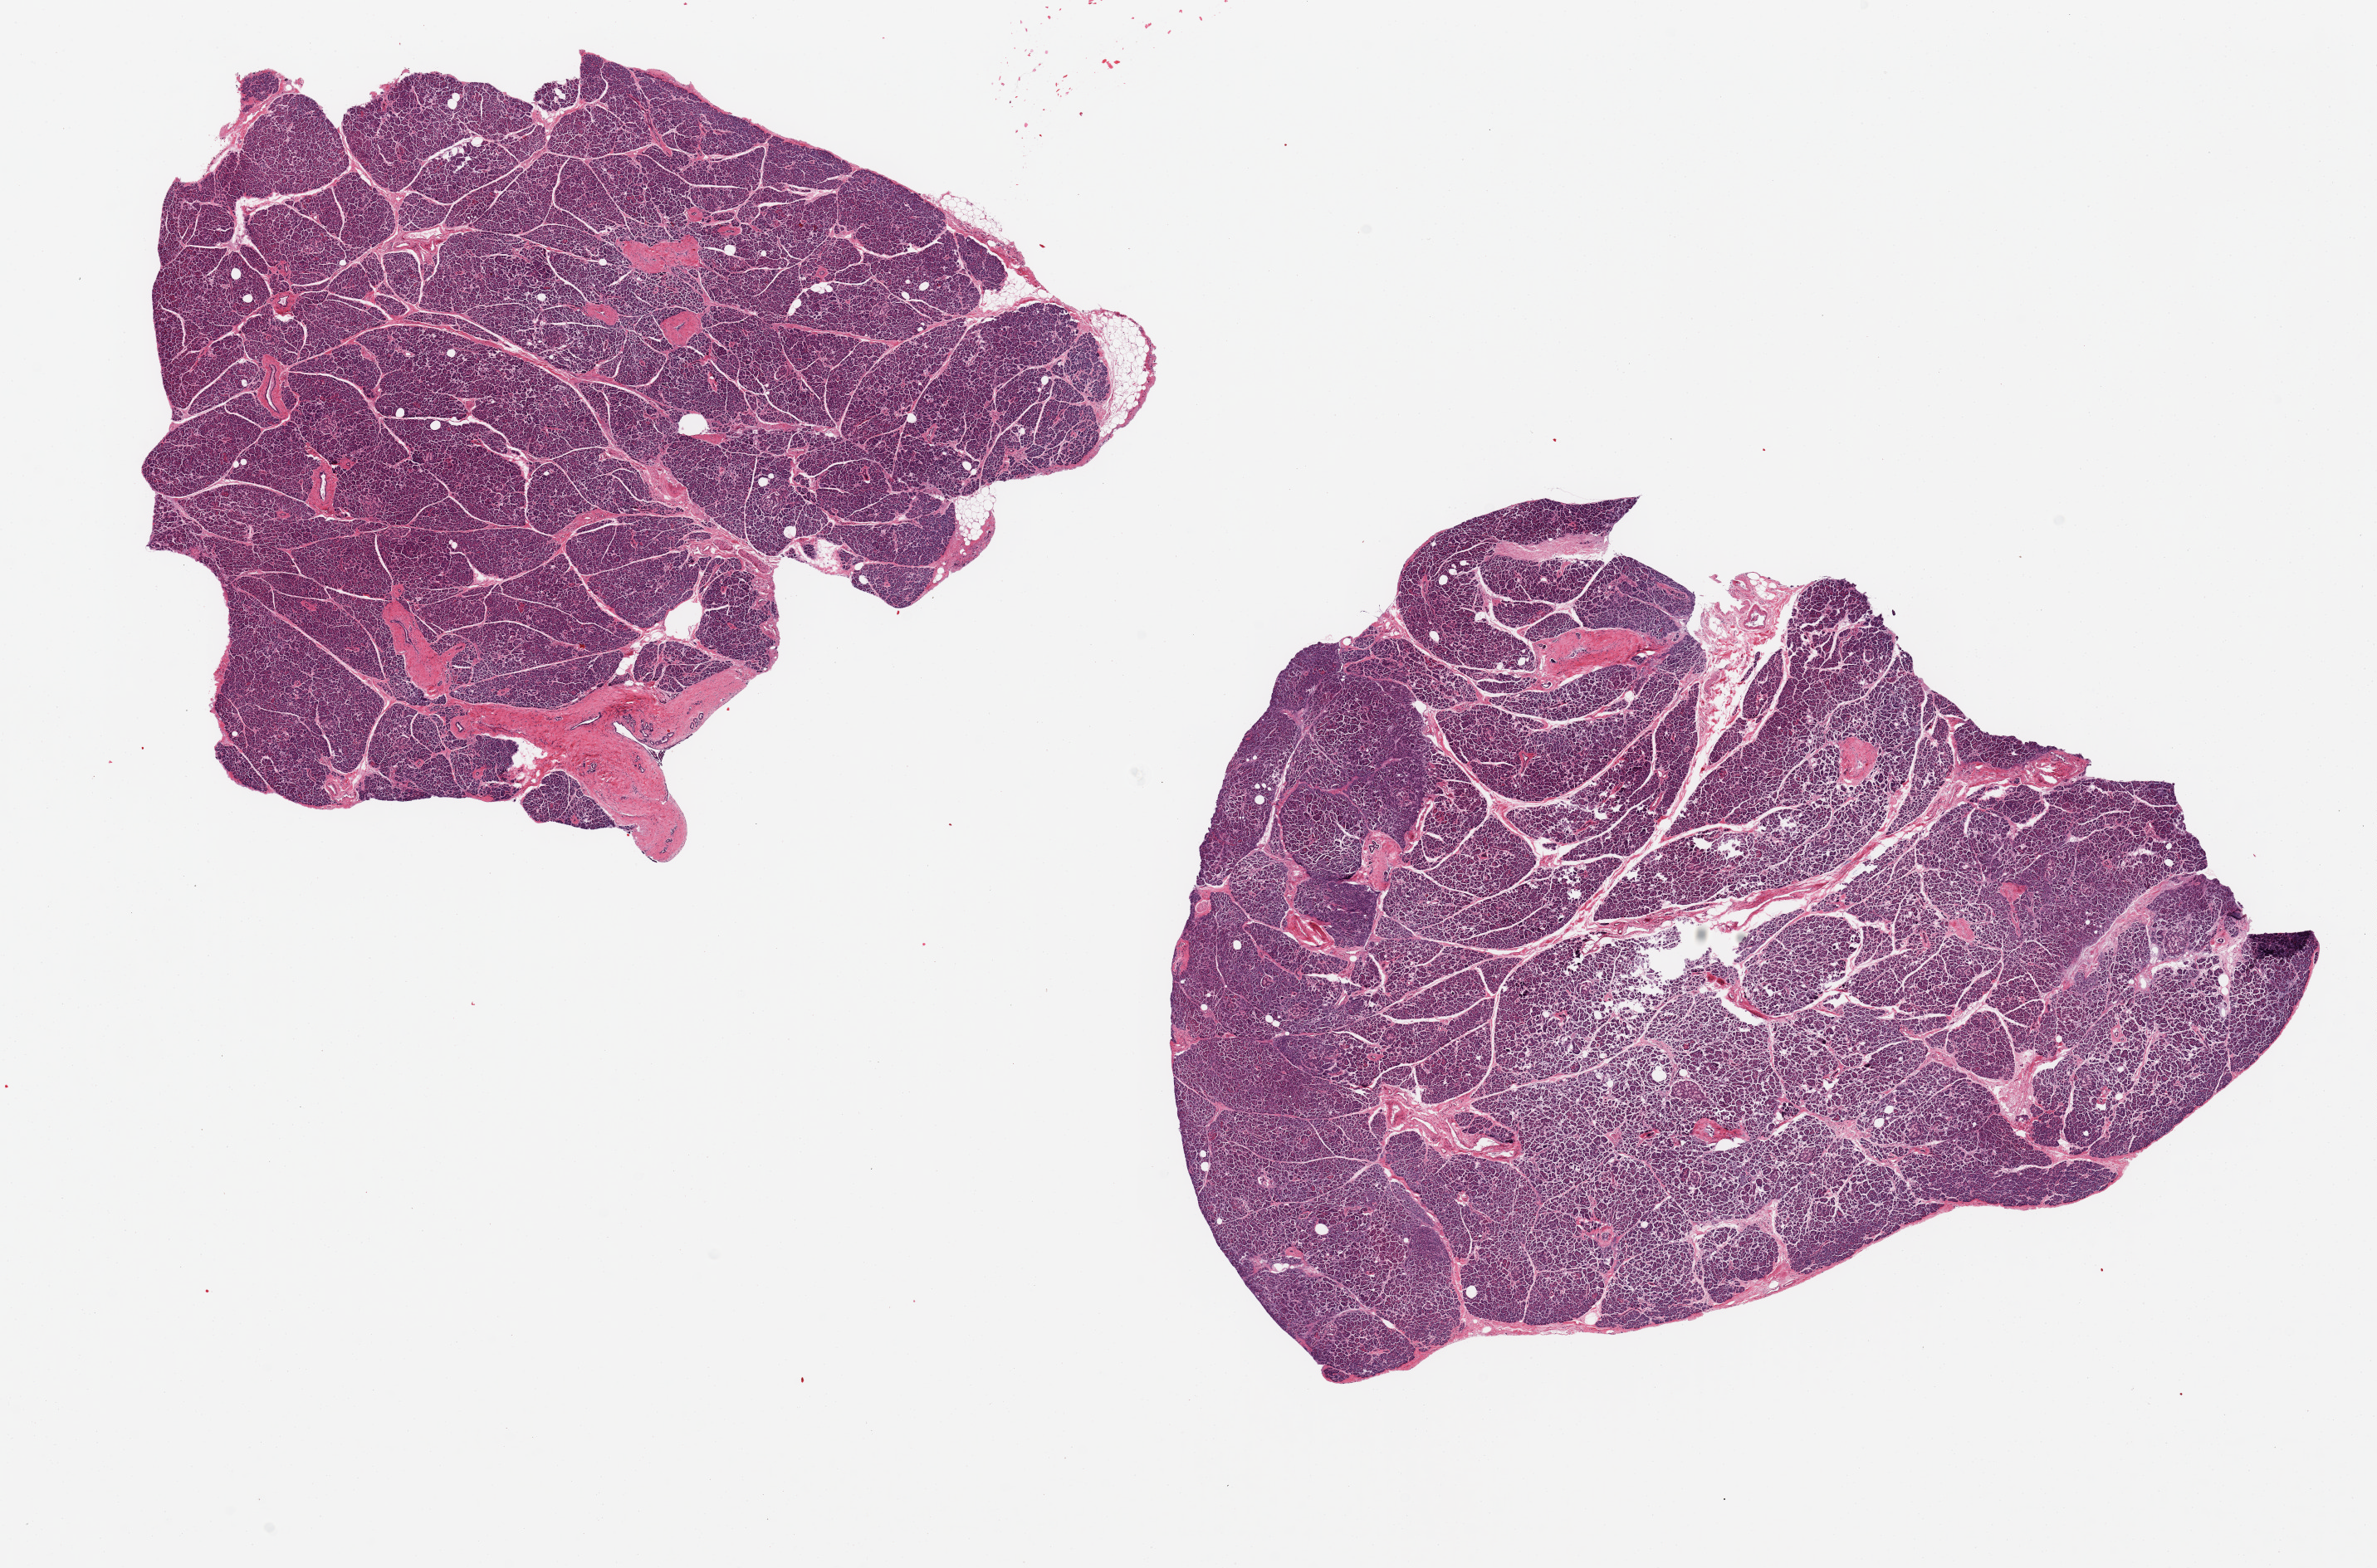
Digitized haematoxylin and eosin-stained section, brightfield, a low-resolution overview of the entire scanned area, about 22.6 x 14.9 mm, PAXgene-fixed, paraffin-embedded tissue, target tissue: pancreas, donor tissue sample. Male donor.
Pathologist's review note for this sample: 2 pieces ~10x8 mm.